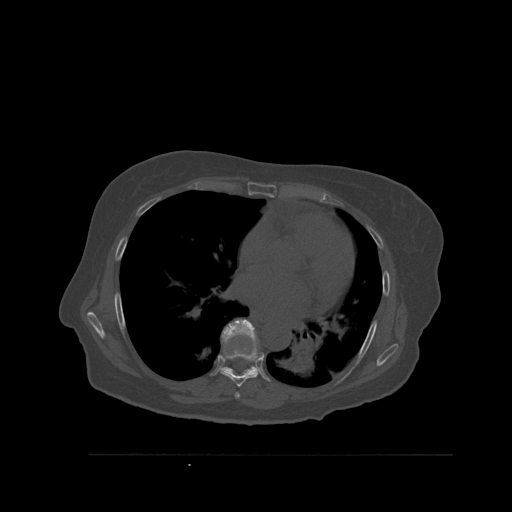
CT including the spine, one axial slice. Position 361 of 527 along the scan axis. Bone window (W 1800 / L 400 HU). 1.5 mm slice thickness. 512 × 512 image matrix, field of view 470 × 470 mm. Female patient, age 73 years. Case-level facts recorded for this patient, not image findings: primary cancer: breast; vertebrae with lytic lesions (as recorded): L2.
Outlined on this slice (semi-automatic segmentation, software-assisted and operator-edited):
- T6 vertebra: box from (x=235, y=392) to (x=240, y=399) px
- T7 vertebra: (x=220, y=339)–(x=261, y=387)
- T8 vertebra: (x=221, y=319)–(x=257, y=375)